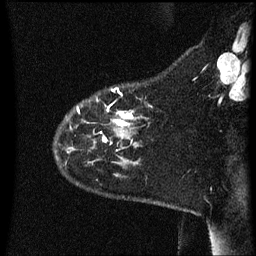
Breast MRI (dynamic contrast-enhanced), one sagittal slice. Slice 11 of 60 in the series (ordered by position). Dynamic contrast-enhanced series, image 2 of 3 at this slice position (ordered by acquisition). 1.5 T. TE 4.2 ms, TR 8.4 ms. 2.2 mm slice thickness. 256 × 256 image matrix, field of view 200 × 200 mm. Patient: female, 35 years. From the clinical record (not read from this slice): setting: breast cancer imaged before/during neoadjuvant chemotherapy; receptor status: HER2-positive.
Annotated regions visible in this slice (semi-automatically segmented with operator editing):
- analysis volume of interest (the breast-tissue region the enhancement analysis was run in; not a lesion): bounding box (x1, y1, x2, y2) in pixels: (57, 90, 148, 163)
- tumour enhancement mask (voxels above the 70 % enhancement threshold inside the analysis volume of interest): (105, 112, 134, 141)